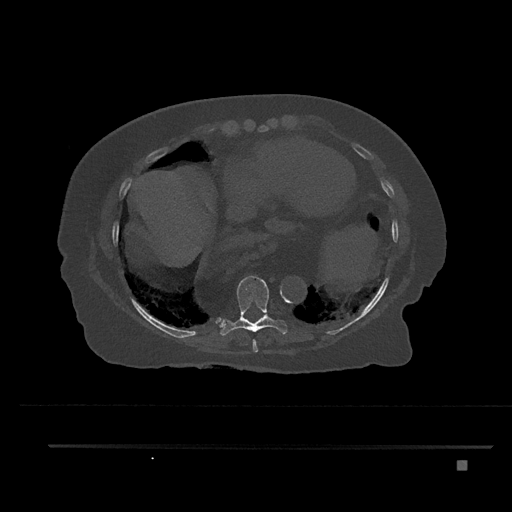
CT including the spine, one axial slice. Position 402 of 797 along the scan axis. Reconstruction kernel Br40s/3. 120 kVp. Bone window (W 1800 / L 400 HU). 0.5 mm slice thickness. 512 × 512 image matrix. Patient: female, 76 years. From the clinical record (not read from this slice): primary cancer: lung; vertebrae with lytic lesions (as recorded): T11, L3.
Structures marked on this image (semi-automatic segmentation, software-assisted and operator-edited):
- T8 vertebra: bounding box [x1, y1, x2, y2] px = [252, 339, 259, 352]
- T9 vertebra: [219, 276, 287, 336]